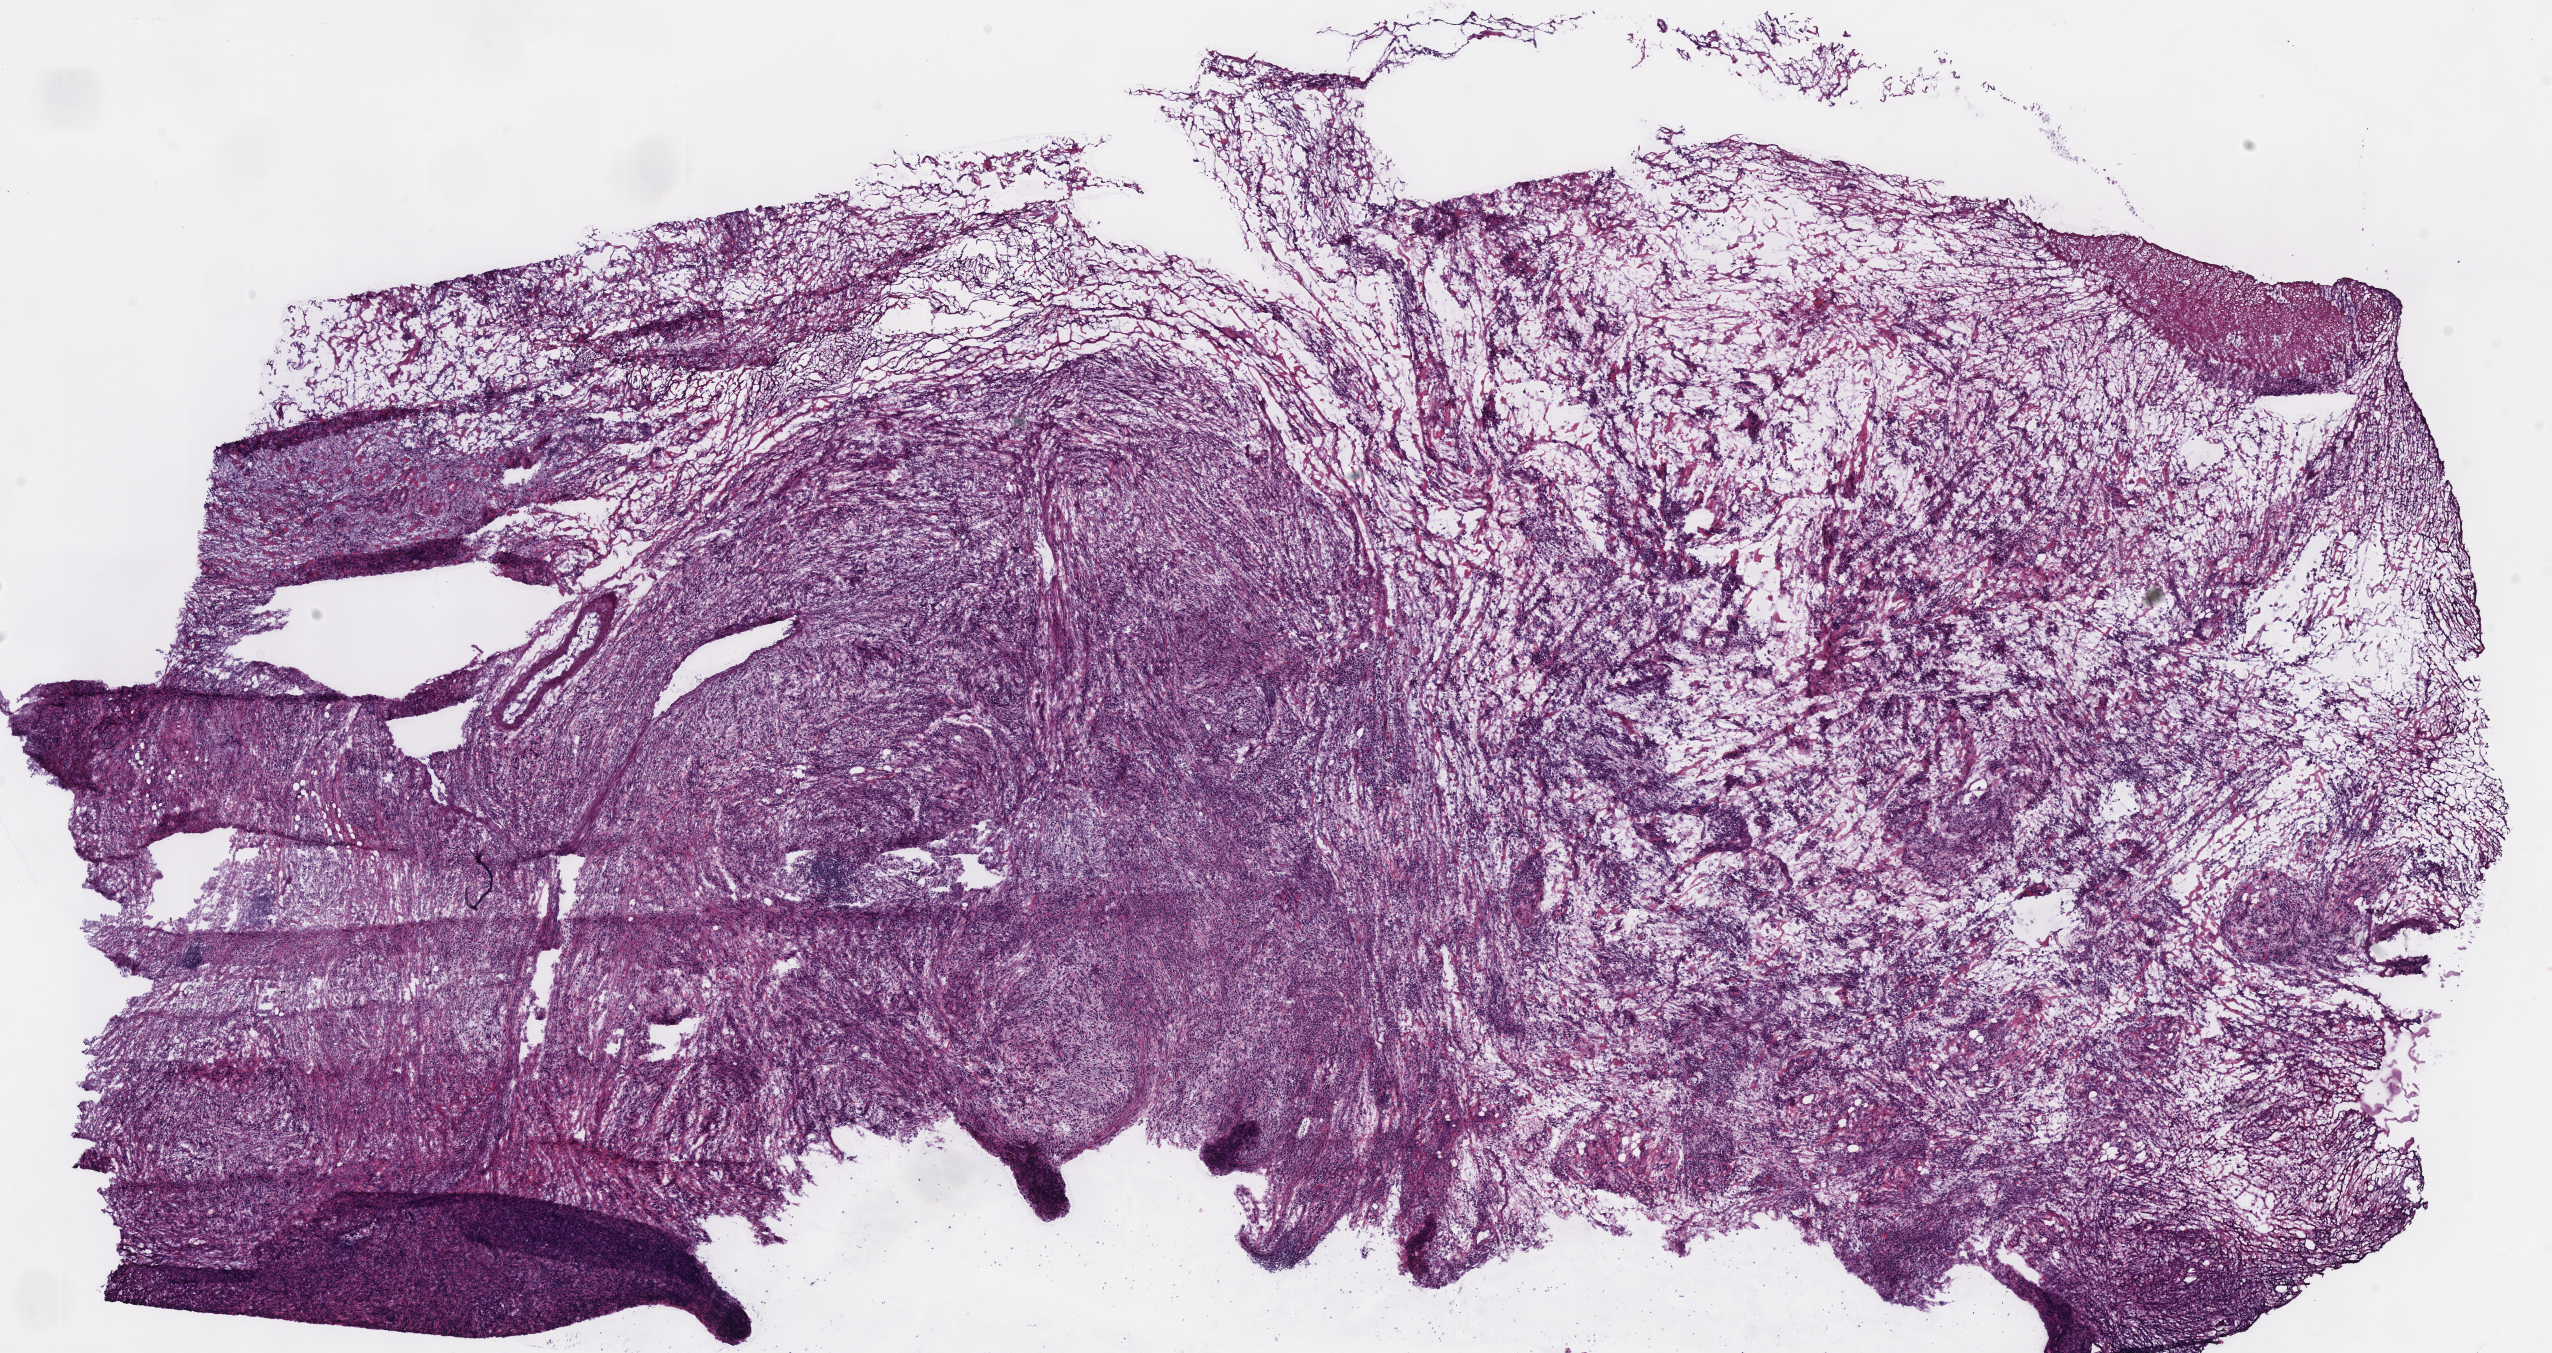
Whole-slide histology image, H&E — a low-resolution overview of the entire scanned area, about 20.1 x 10.6 mm, frozen section from the bottom of the tissue portion, sample: primary tumour, stomach. Patient: male, age at initial diagnosis 61 years. Histologic grade: GX (grade cannot be assessed). Pathologist review of this section (percent, as recorded): tumour cells 80%, tumour nuclei 75%, normal cells 0%, stromal cells 20%, necrosis 0%.
• pathologic diagnosis: Carcinoma, diffuse type
• AJCC pathologic stage: IIB (7th edition)
• lymph nodes positive (case pathology): 1 of 6 examined